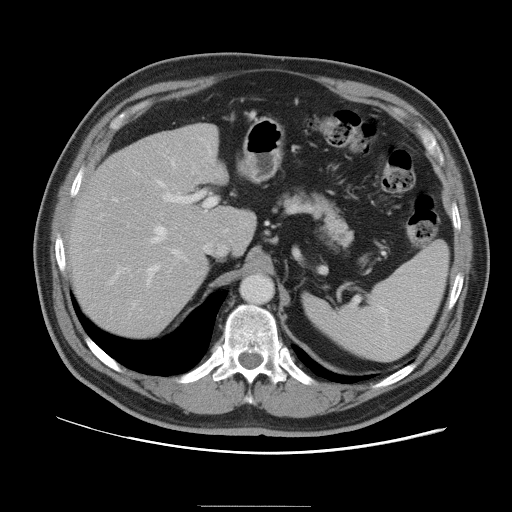
Contrast-enhanced abdominal CT, one axial slice. Position 68 of 105 along the scan axis. Intravenous contrast given. Soft-tissue window (W 400 / L 40 HU). 5 mm slice thickness. 512 × 512 image matrix, field of view 399 × 399 mm. Male patient, age 64 years. Case-level facts recorded for this patient, not image findings: diagnosis: colorectal cancer liver metastases, imaged before liver resection; multiple liver metastases: yes; largest metastasis: 3 cm; disease in both lobes: yes.
Annotated regions visible in this slice (outlined manually by an expert reader):
- hepatic veins: bounding box [x1, y1, x2, y2] px = [148, 162, 180, 280]
- liver: [69, 125, 256, 339]
- planned liver remnant (the part of the liver to remain after resection): [69, 139, 256, 339]
- portal vein (with intrahepatic branches): [110, 192, 216, 284]